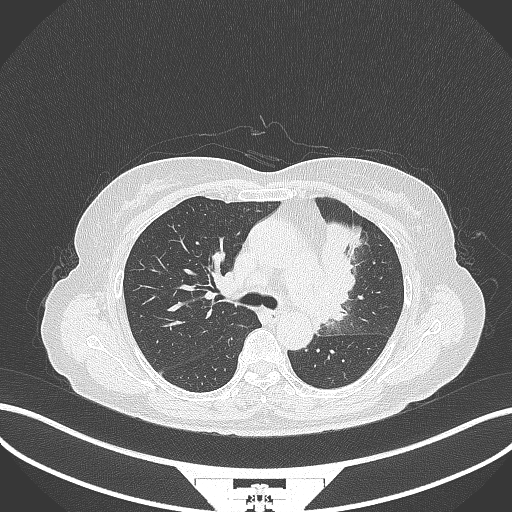
Chest CT, one axial slice. Slice 218 of 382 in the series (ordered by position). Lung window (W 1500 / L -600 HU). 512 × 512 image matrix, field of view 400 × 400 mm. Patient: female, 64 years. From the clinical record (not read from this slice): clinical TNM (as recorded): T2a N2 M0.
Annotated regions visible in this slice (bounding box drawn by a radiologist):
- lung tumour (recorded histology: adenocarcinoma): bounding box (x1, y1, x2, y2) in pixels: (313, 220, 361, 332)